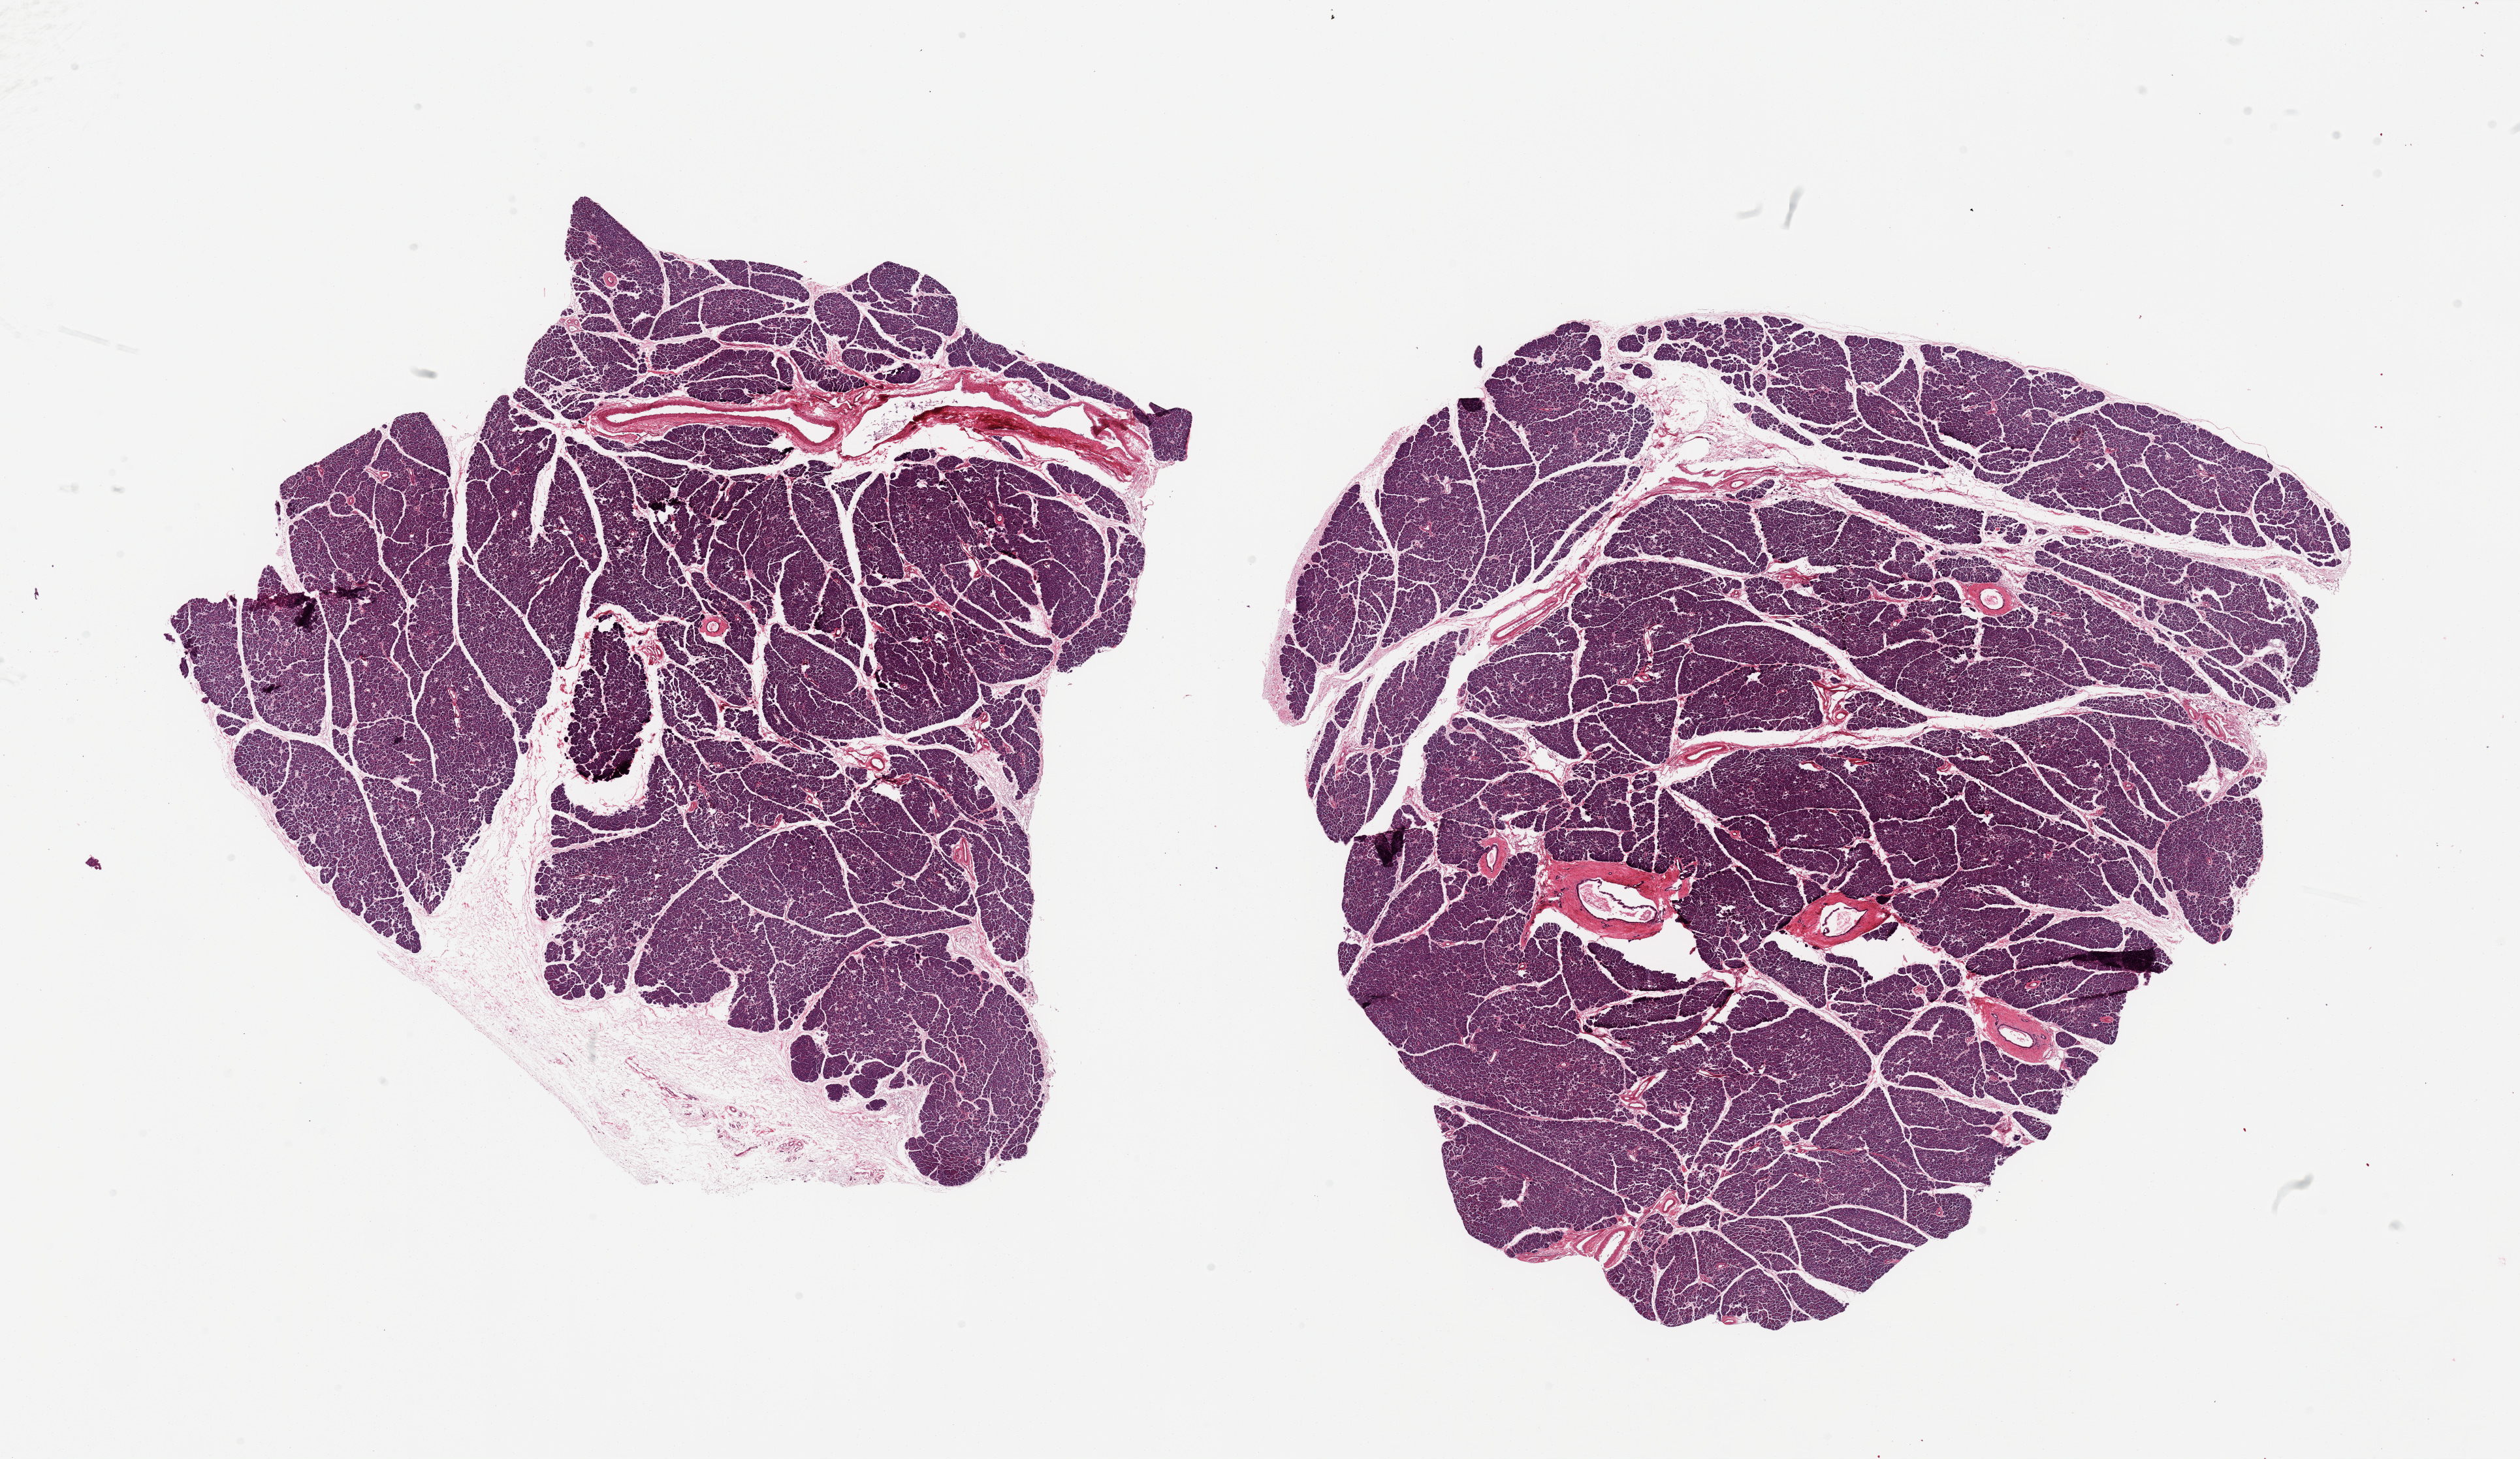
Digitized hematoxylin and eosin (H&E)-stained section — shown as a low-resolution overview of the whole scanned area (about 30.5 x 17.7 mm), PAXgene-fixed, paraffin-embedded tissue, target tissue: pancreas, tissue donor sample. Donor sex: female.
* reviewer comment on this tissue sample: 2 pieces; over-sized